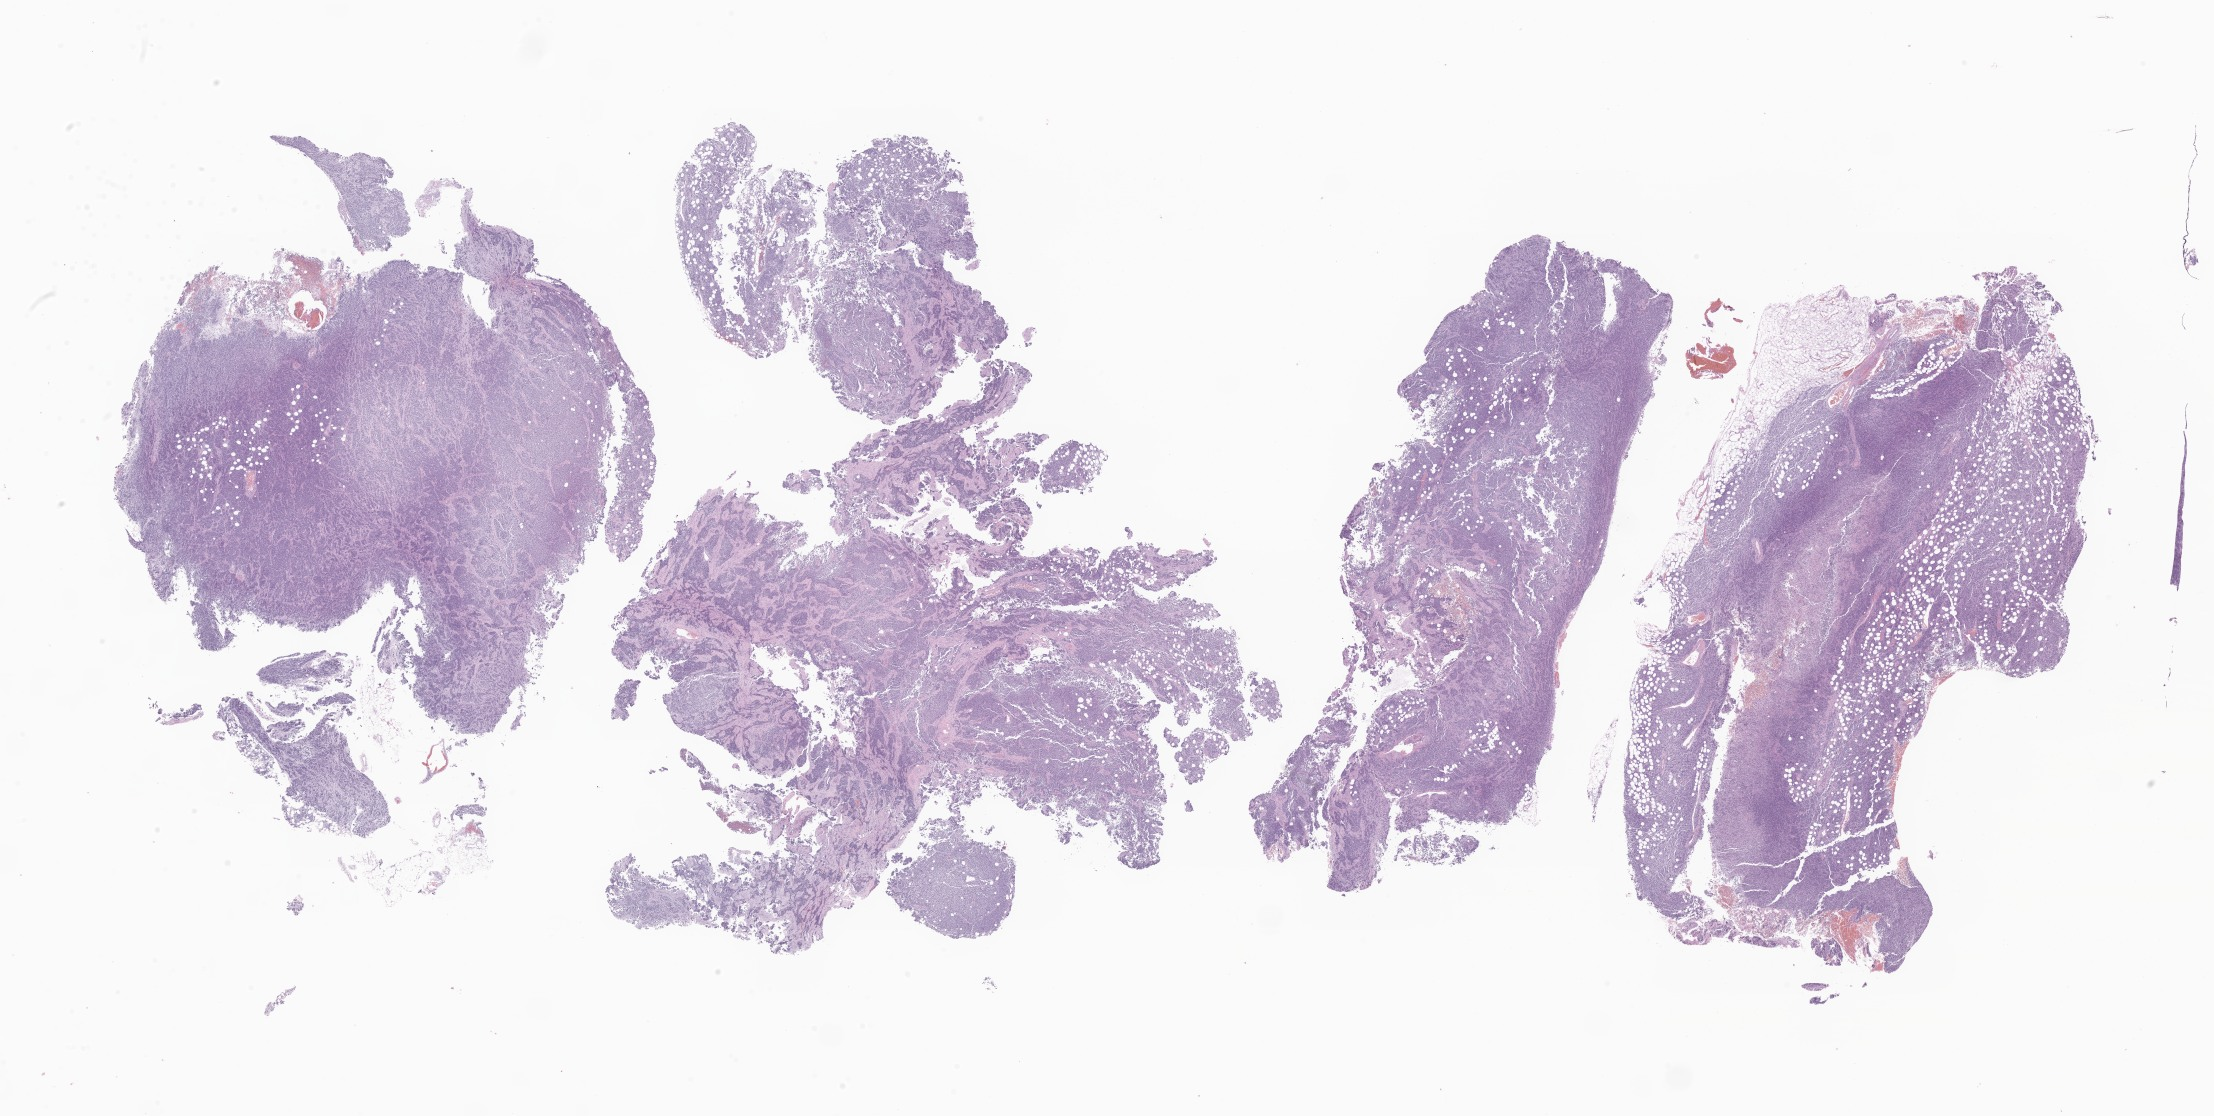
Whole-slide image, haematoxylin and eosin stain of tumor tissue from the vertebral column, whole scanned area (about 37.3 x 18.8 mm) shown as a low-resolution overview. Formalin-fixed paraffin-embedded section. Patient female; age 205 months (17 years 1 month).
Diagnosis: Alveolar rhabdomyosarcoma.